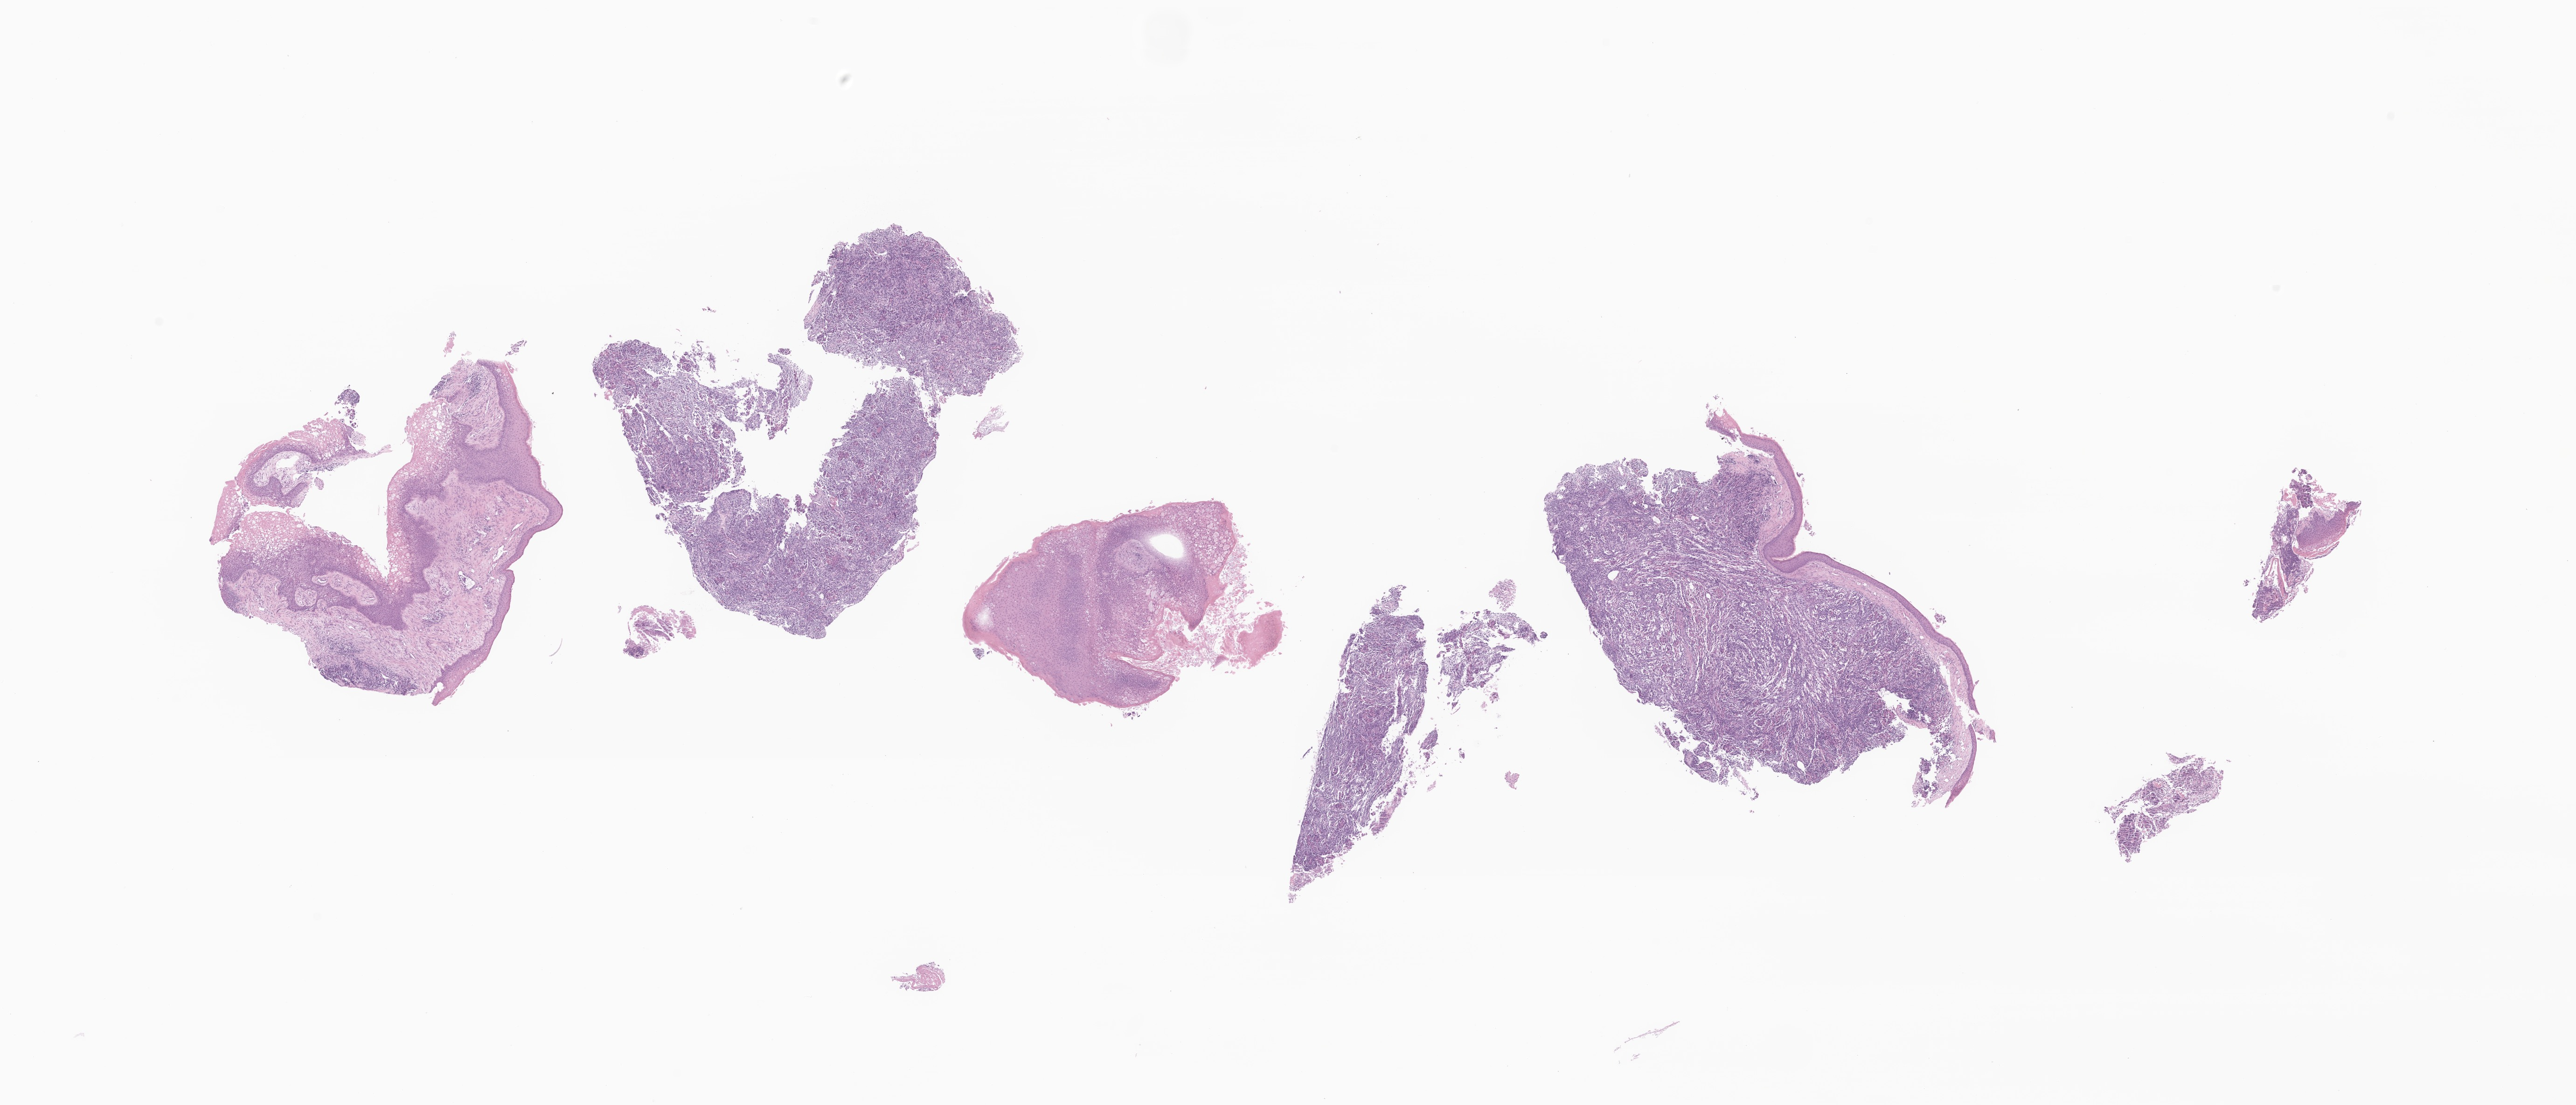
Haematoxylin and eosin whole-slide image of tumor tissue from the middle ear, a low-resolution overview of the entire scanned area, about 23.3 x 10.0 mm, formalin-fixed, paraffin-embedded (FFPE) tissue. Patient: male, age 687 days (about 1.9 years).
- diagnosis: Embryonal rhabdomyosarcoma, NOS